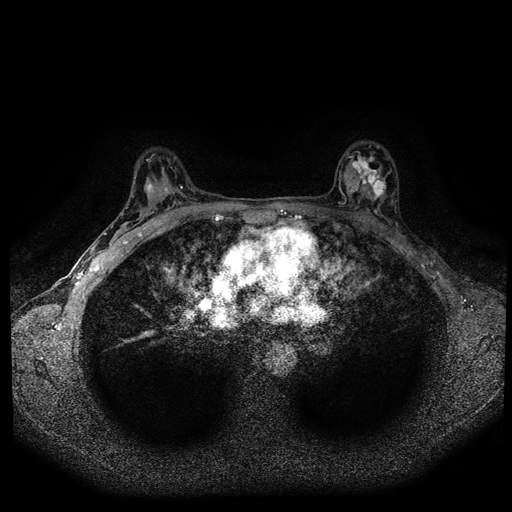
Breast MRI (dynamic contrast-enhanced, multi-phase), one axial slice. Slice 59 of 108 in the series (ordered by position). Dynamic contrast-enhanced series, time point 2 of 5 at this slice position (early post-contrast). 1.5 T. TE 2.7 ms, TR 5.5 ms. 512 × 512 image matrix, field of view 320 × 320 mm. Female patient, age 36 years.
Outlined on this slice (semi-automatic segmentation, software-assisted and operator-edited):
- breast lesion (labelled 'tumour' in the annotation; benign lesions carry a separate 'benign' label): bounding box <343,151,387,205> (left, top, right, bottom; pixels)